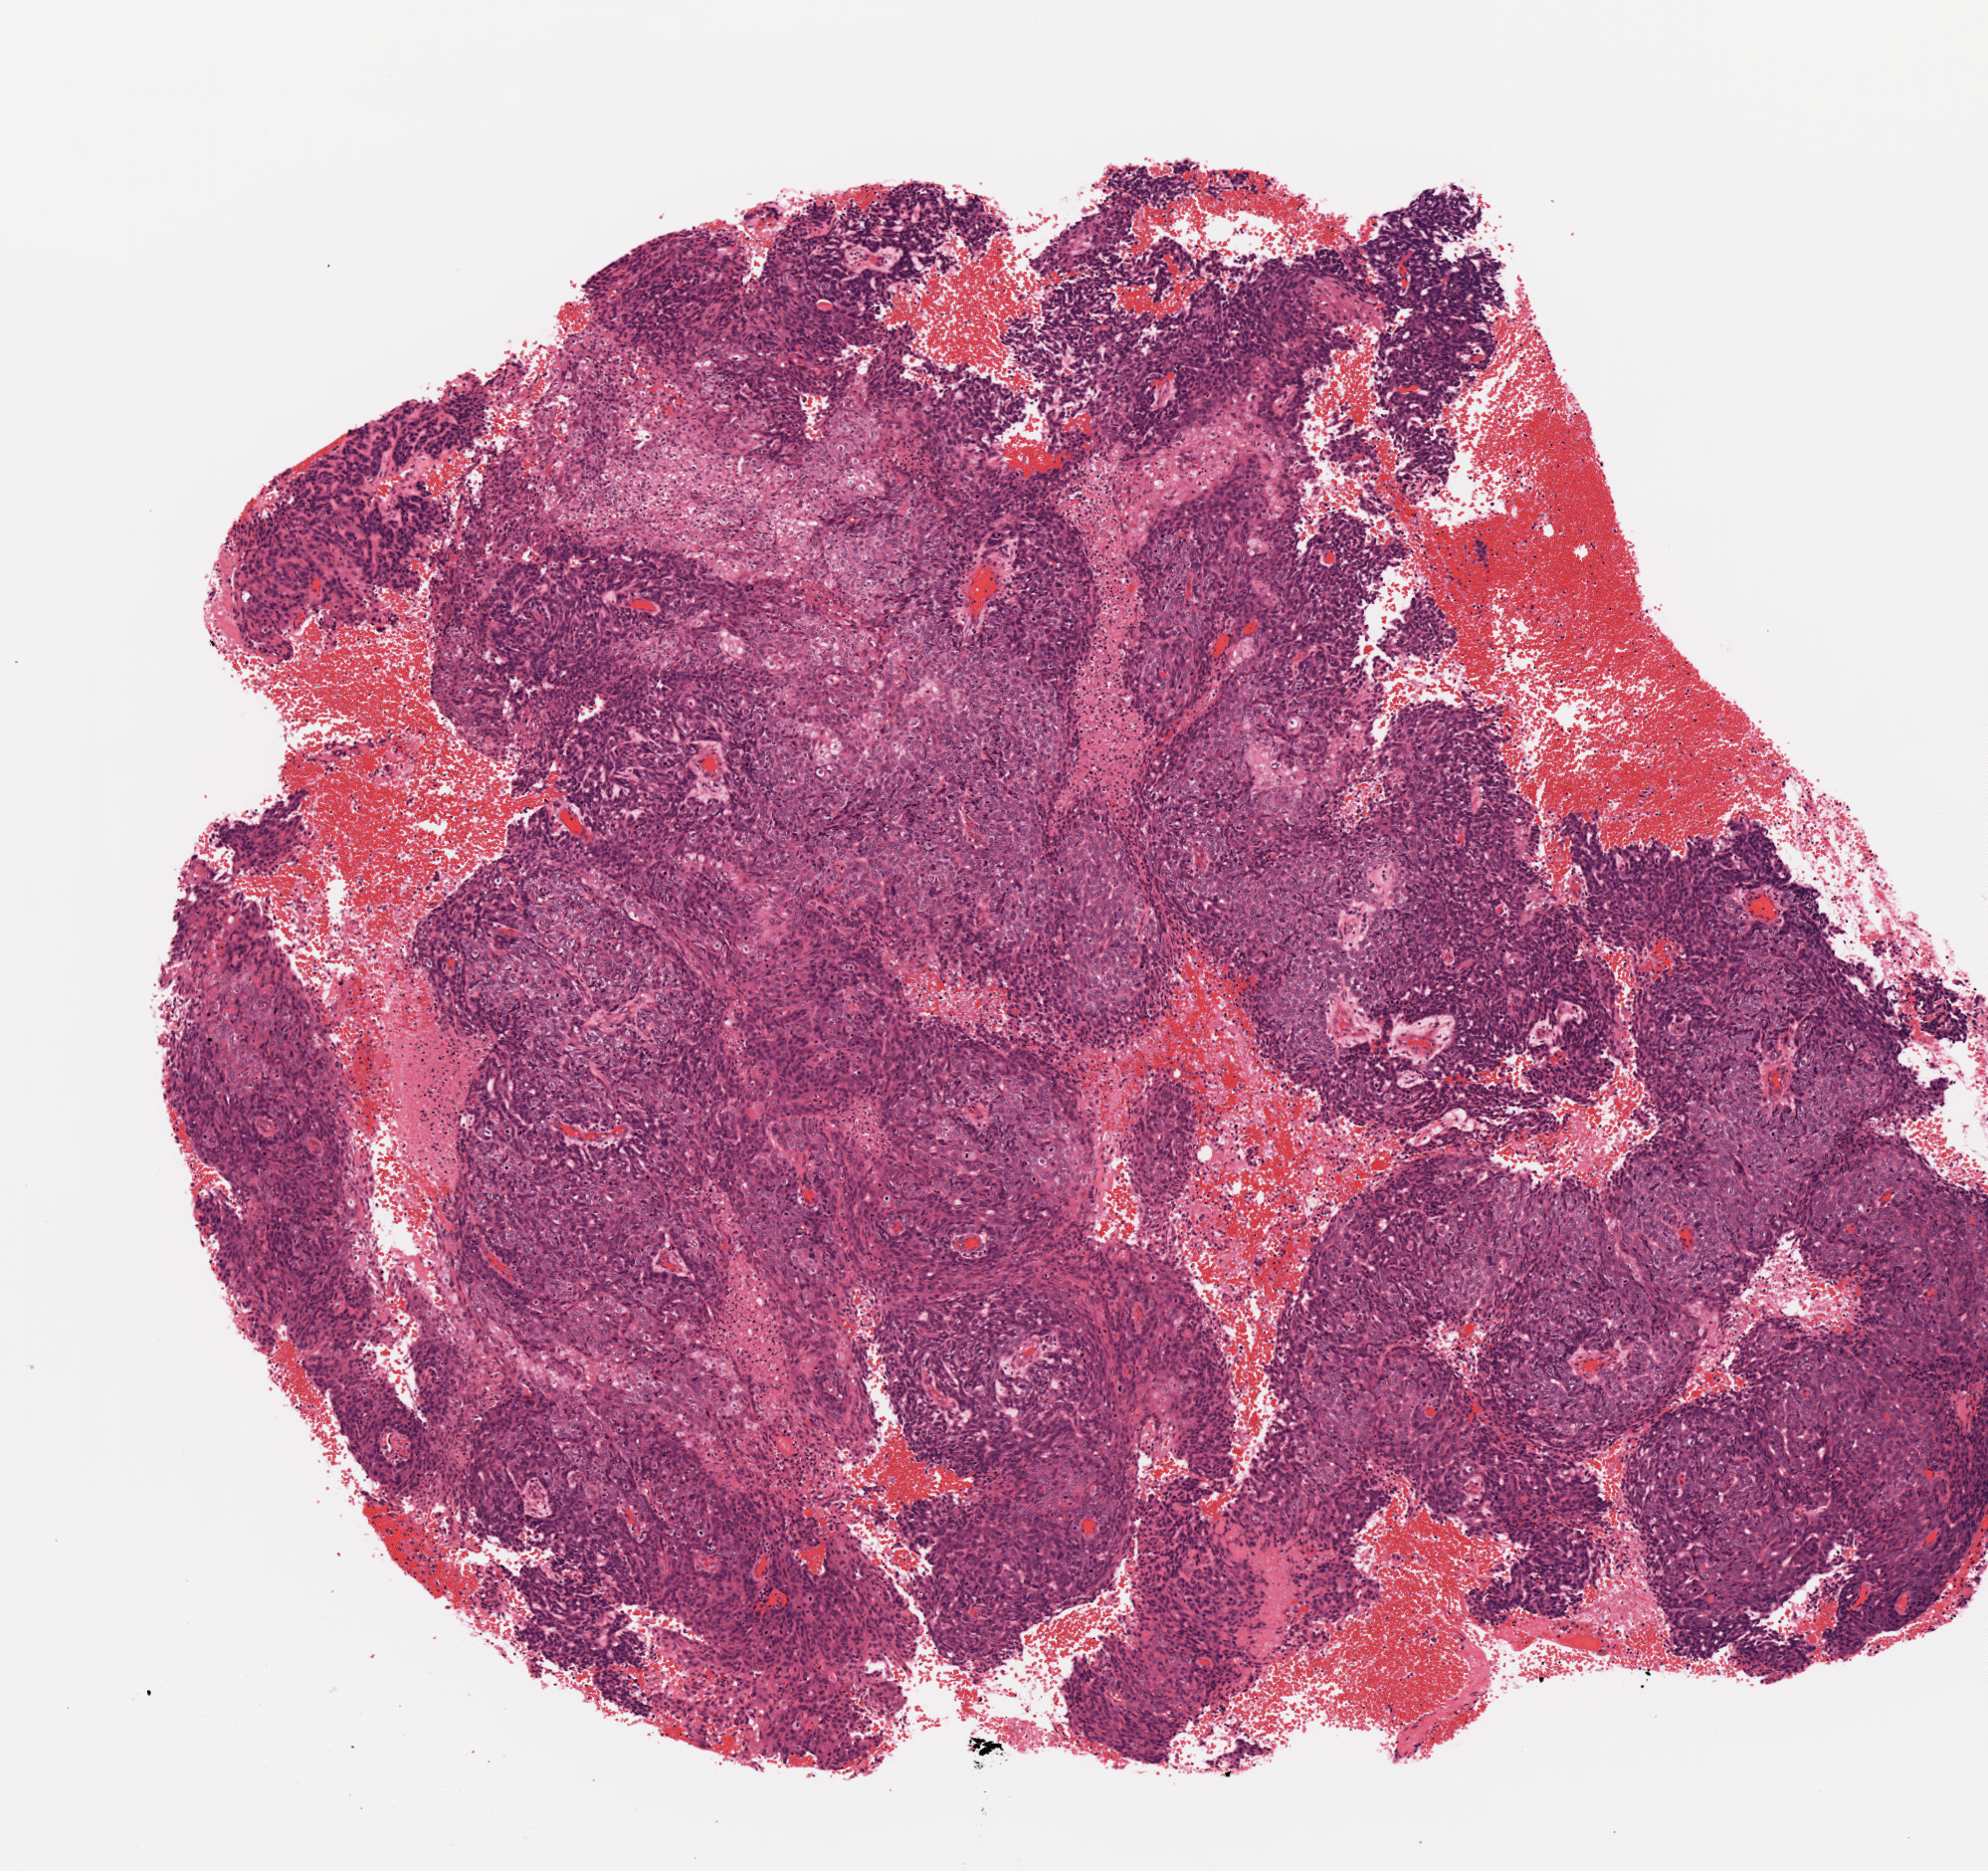
Hematoxylin and eosin (H&E) stained whole-slide image, shown as a low-resolution overview of the whole scanned area (about 4.0 x 3.8 mm, slide scanned at 20x); FFPE section; sample: primary tumour, lung. Male patient; age at initial diagnosis 68 years.
• pathologic diagnosis: Squamous cell carcinoma, NOS
• TNM: T1 N0 M0
• AJCC pathologic stage: IA (6th edition)